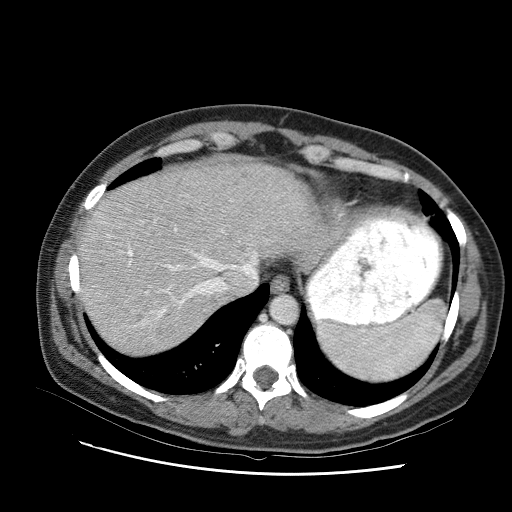
Contrast-enhanced abdominal CT (liver protocol), one axial slice; slice 78 of 95 in the series (ordered by position); 120 kVp; one of 2 acquisitions stored at this slice position; soft-tissue window (W 400 / L 40 HU); 2.5 mm slice thickness; 512 × 512 image matrix, field of view 360 × 360 mm. From the clinical record (not read from this slice): diagnosis: hepatocellular carcinoma (patient treated with transarterial chemoembolisation; whether this scan precedes or follows treatment is not stated here); TNM stage (as recorded): Stage-I; Child-Pugh class: B.
Structures marked on this image (semi-automatic segmentation, software-assisted and operator-edited):
- liver parenchyma outside the tumour (the mass and vessels are separate outlines, so this box may not span the whole liver): bounding box [x1, y1, x2, y2] px = [78, 156, 308, 332]
- liver vessels: [115, 229, 175, 292]